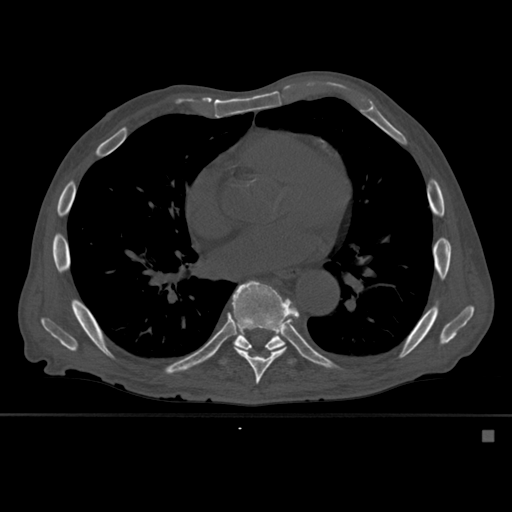
CT including the spine, one axial slice; slice 344 of 527 in the series (ordered by position); bone window (W 1800 / L 400 HU); 1.5 mm slice thickness; 512 × 512 image matrix. Patient: male, 78 years. Case-level facts recorded for this patient, not image findings: primary cancer: prostate.
Outlined on this slice (semi-automatically segmented with operator editing):
- T8 vertebra: bounding box [x1, y1, x2, y2] px = [227, 280, 300, 385]
- T9 vertebra: [222, 297, 294, 365]